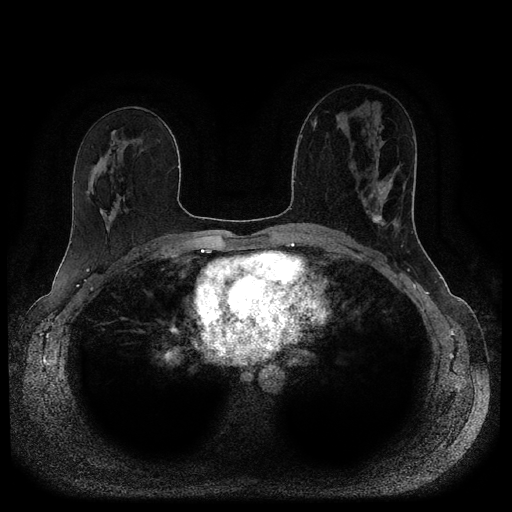
Breast MRI (dynamic contrast-enhanced, multi-phase), one axial slice; slice 55 of 116 in the series (ordered by position); dynamic contrast-enhanced series, time point 2 of 5 at this slice position (early post-contrast); 1.5 T; TE 2.6 ms, TR 5.3 ms; 512 × 512 image matrix, field of view 350 × 350 mm. Patient: female, 45 years.
Annotated regions visible in this slice (semi-automatically segmented with operator editing):
- breast lesion (labelled 'tumour' in the annotation; benign lesions carry a separate 'benign' label): bounding box <370,174,401,230> (left, top, right, bottom; pixels)